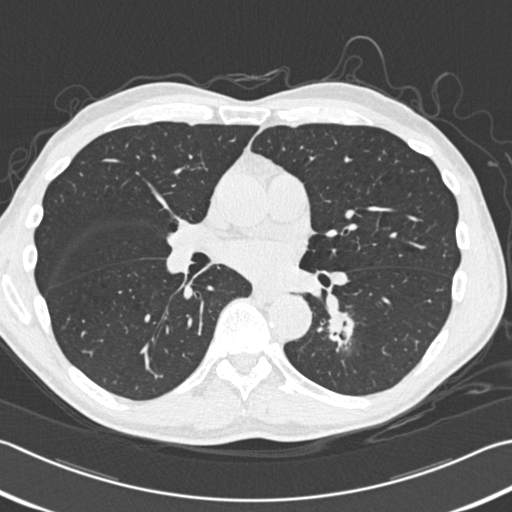
Low-dose screening chest CT, one axial slice. Position 183 of 354 along the scan axis. Reconstruction kernel B30f. 120 kVp. Lung window (W 1500 / L -600 HU). 1 mm slice thickness. 512 × 512 image matrix, field of view 346 × 346 mm.
Structures marked on this image (manually delineated by an expert):
- lesion 1 (tumor, lower lobe of left lung): bounding box <328,312,351,336> (left, top, right, bottom; pixels)